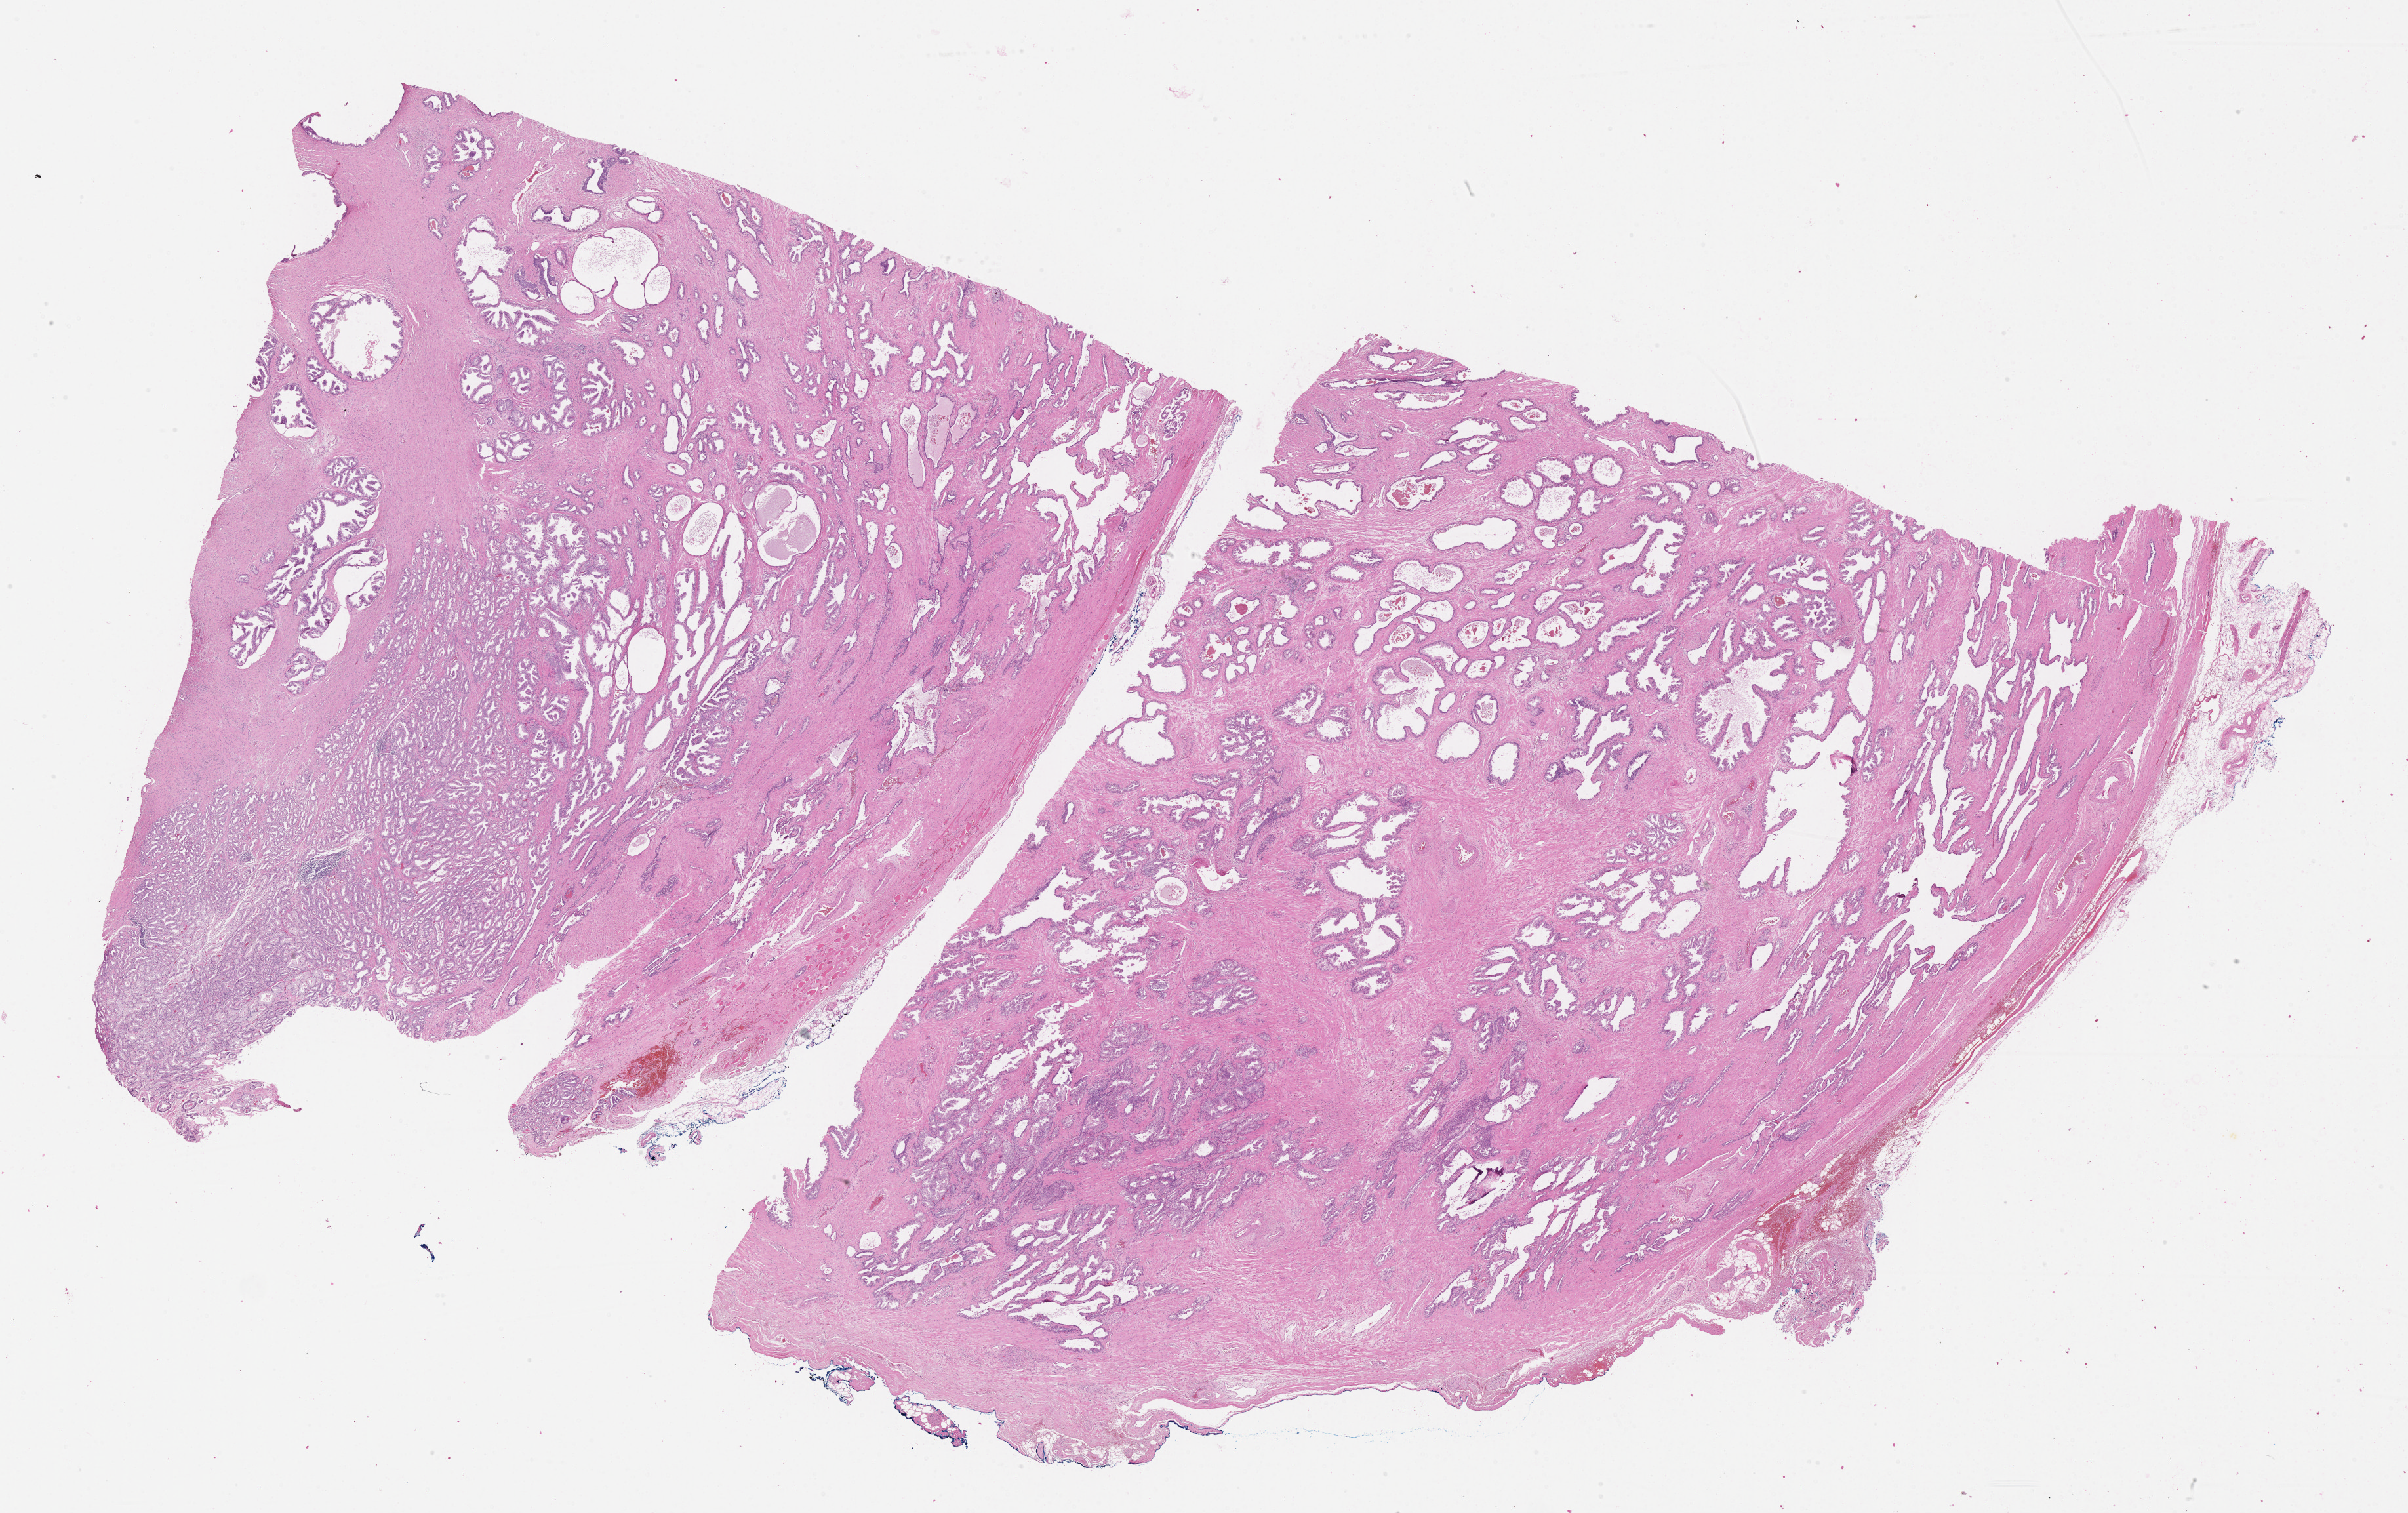
Whole-slide histology image, H&E, low-resolution overview of the scanned area, about 29.7 x 18.7 mm (acquisition: 40x scan), formalin-fixed paraffin-embedded (FFPE) diagnostic section, sample: primary tumour, prostate. Male patient; age at initial diagnosis 59 years. Gleason score: 6 (3+3).
• laterality: bilateral
• histologic diagnosis: Adenocarcinoma, NOS (prostate gland)